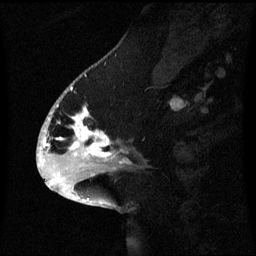
Breast MRI (dynamic contrast-enhanced), one sagittal slice; slice 25 of 60 in the series (ordered by position); dynamic contrast-enhanced series, image 2 of 3 at this slice position (ordered by acquisition); 1.5 T; TE 4.2 ms, TR 8.4 ms; 2.1 mm slice thickness; 256 × 256 image matrix. Female patient, age 53 years. Case-level facts recorded for this patient, not image findings: setting: breast cancer imaged before/during neoadjuvant chemotherapy; receptor status: HR-positive, HER2-negative.
Structures marked on this image (semi-automatic segmentation, software-assisted and operator-edited):
- analysis volume of interest (the breast-tissue region the enhancement analysis was run in; not a lesion): bounding box (x1, y1, x2, y2) in pixels: (52, 90, 131, 171)
- tumour enhancement mask (voxels above the 70 % enhancement threshold inside the analysis volume of interest): (57, 106, 123, 163)